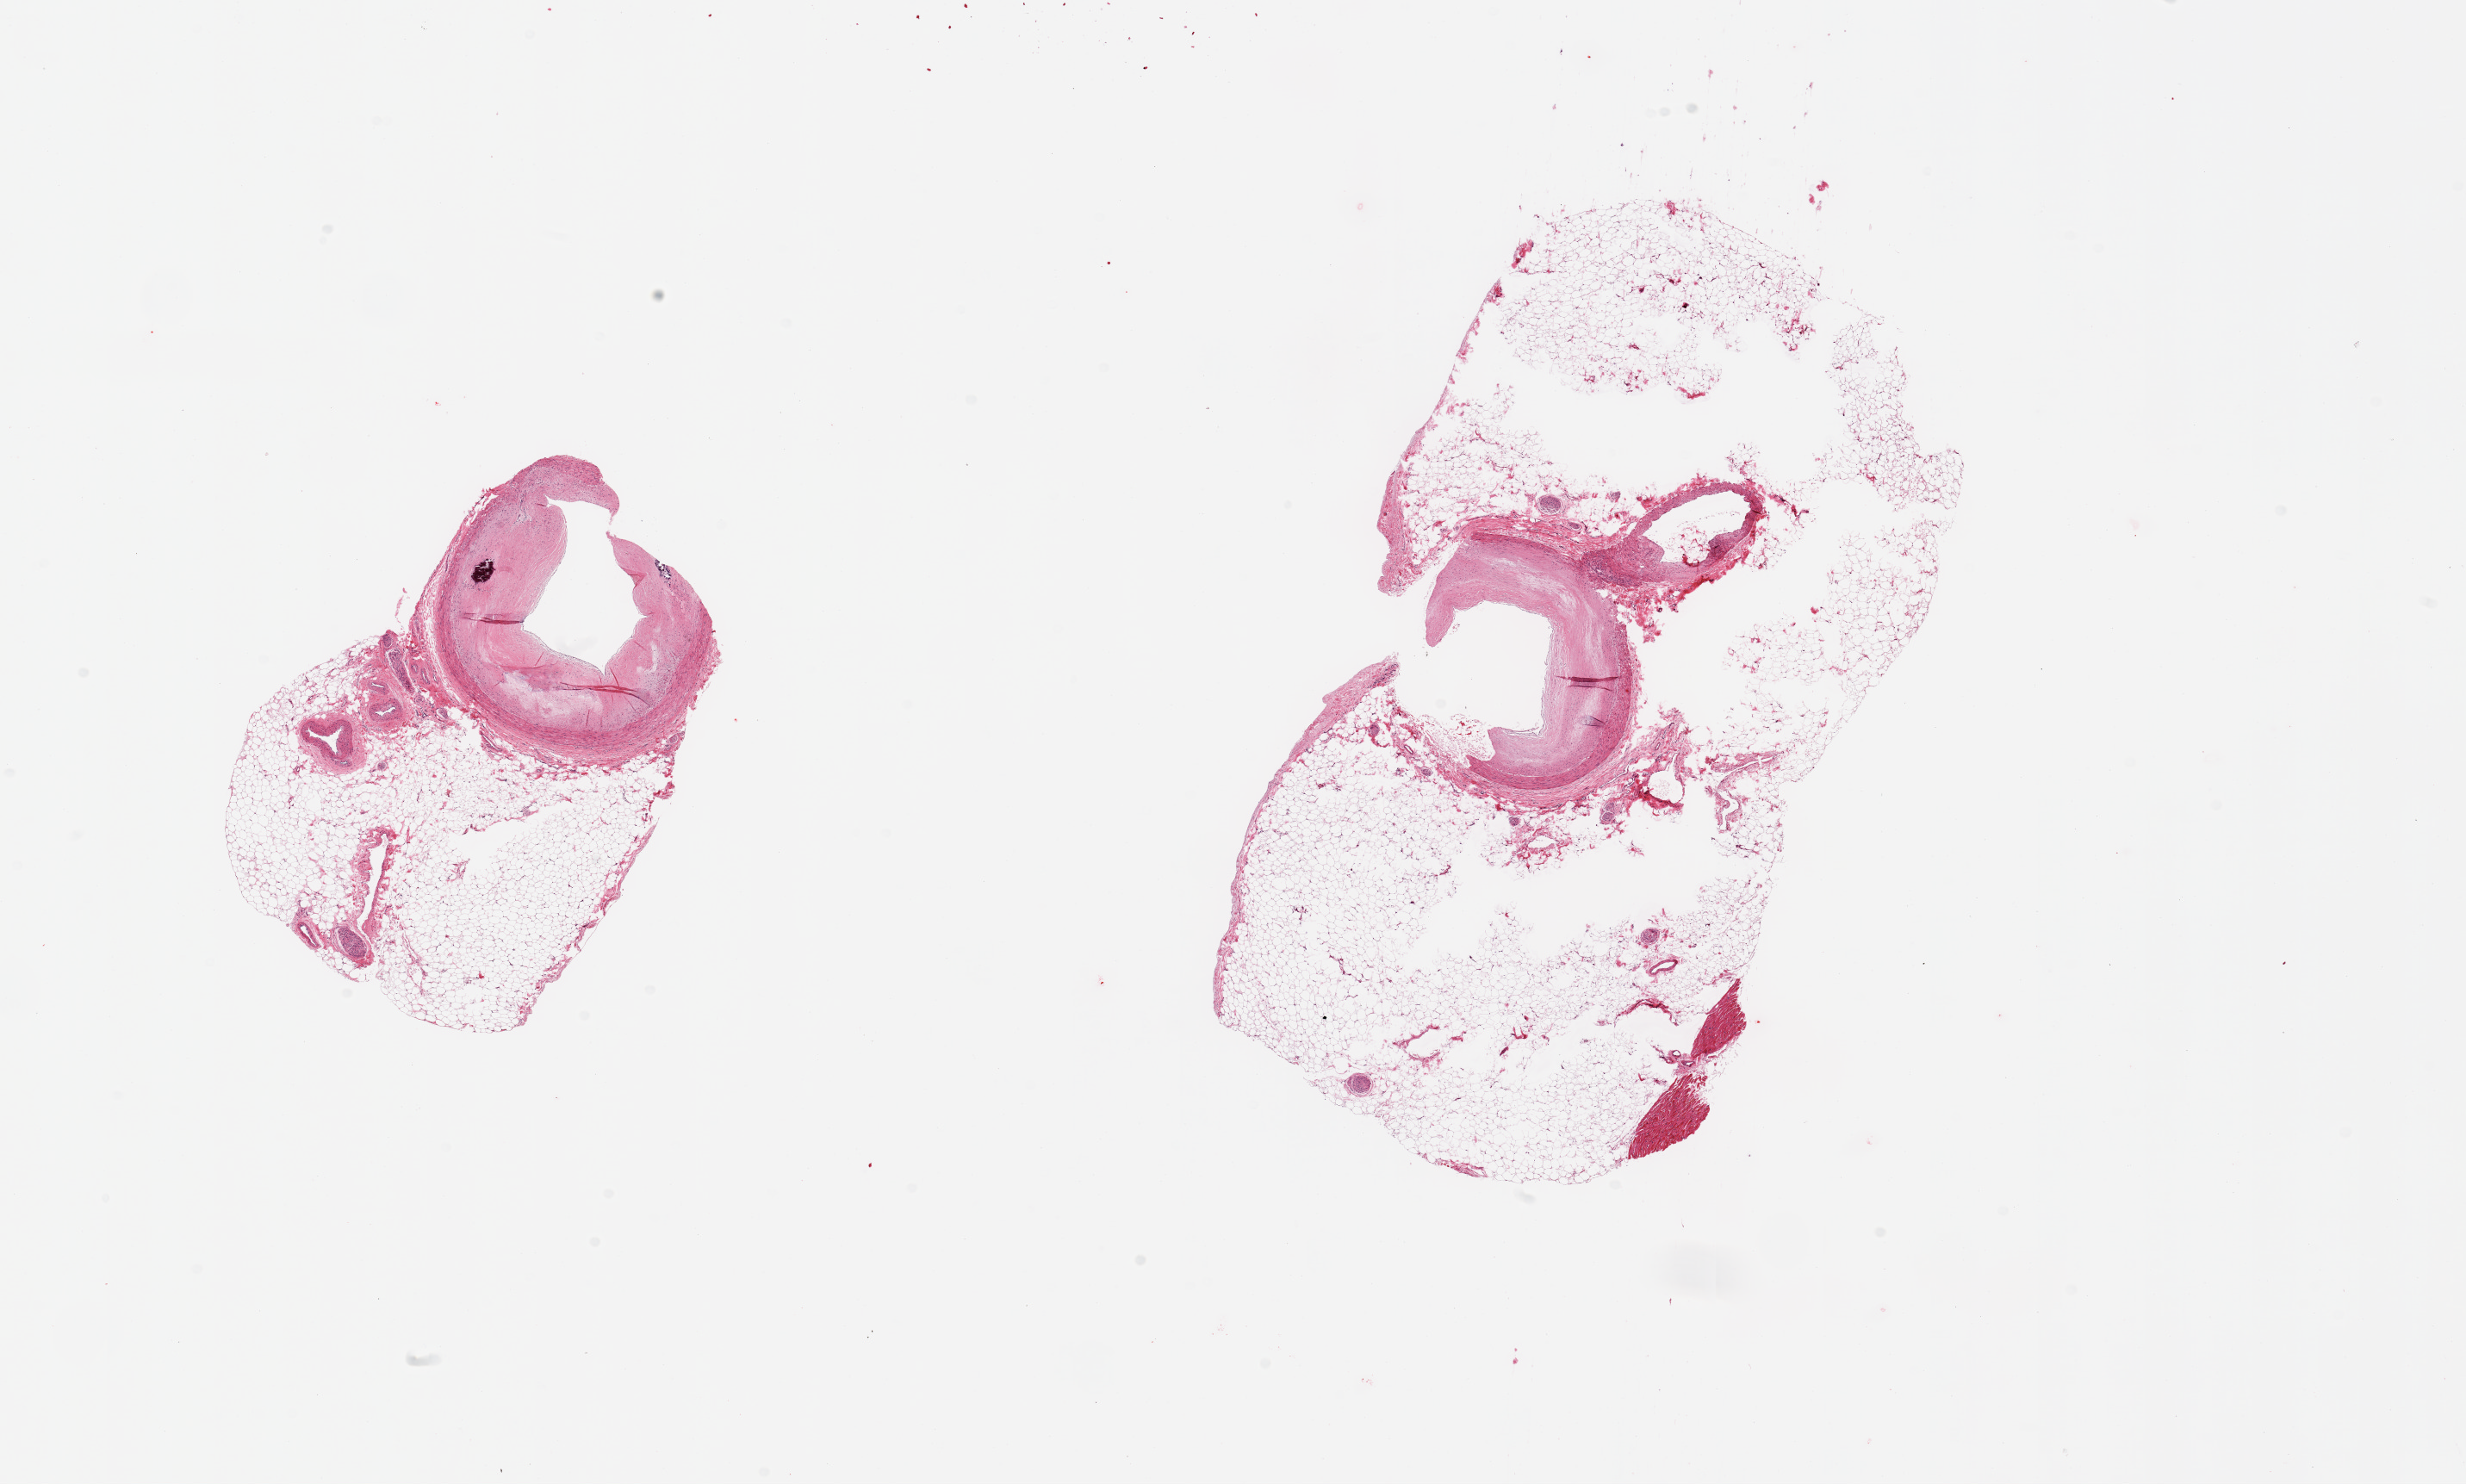
Digitized haematoxylin and eosin-stained section — whole scanned area (about 22.6 x 13.6 mm) shown as a low-resolution overview, PAXgene-fixed, paraffin-embedded tissue, target tissue: coronary artery, donor tissue sample. Donor sex: male.
Review note (as recorded): 2 pieces; calcific atherosclerosis, abundant attached fat (30 and 80%).